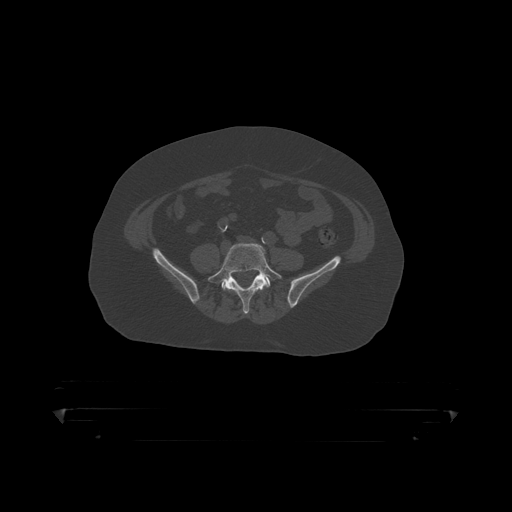
CT including the spine, one axial slice; slice 41 of 390 in the series (ordered by position); reconstruction kernel STANDARD; 120 kVp; bone window (W 1800 / L 400 HU); 1.25 mm slice thickness; 512 × 512 image matrix, field of view 650 × 650 mm. Patient: male, 60 years. From the clinical record (not read from this slice): primary cancer: prostate.
Structures marked on this image (semi-automatically segmented with operator editing):
- L4 vertebra: bounding box [x1, y1, x2, y2] px = [230, 287, 264, 291]
- L5 vertebra: [208, 243, 283, 314]